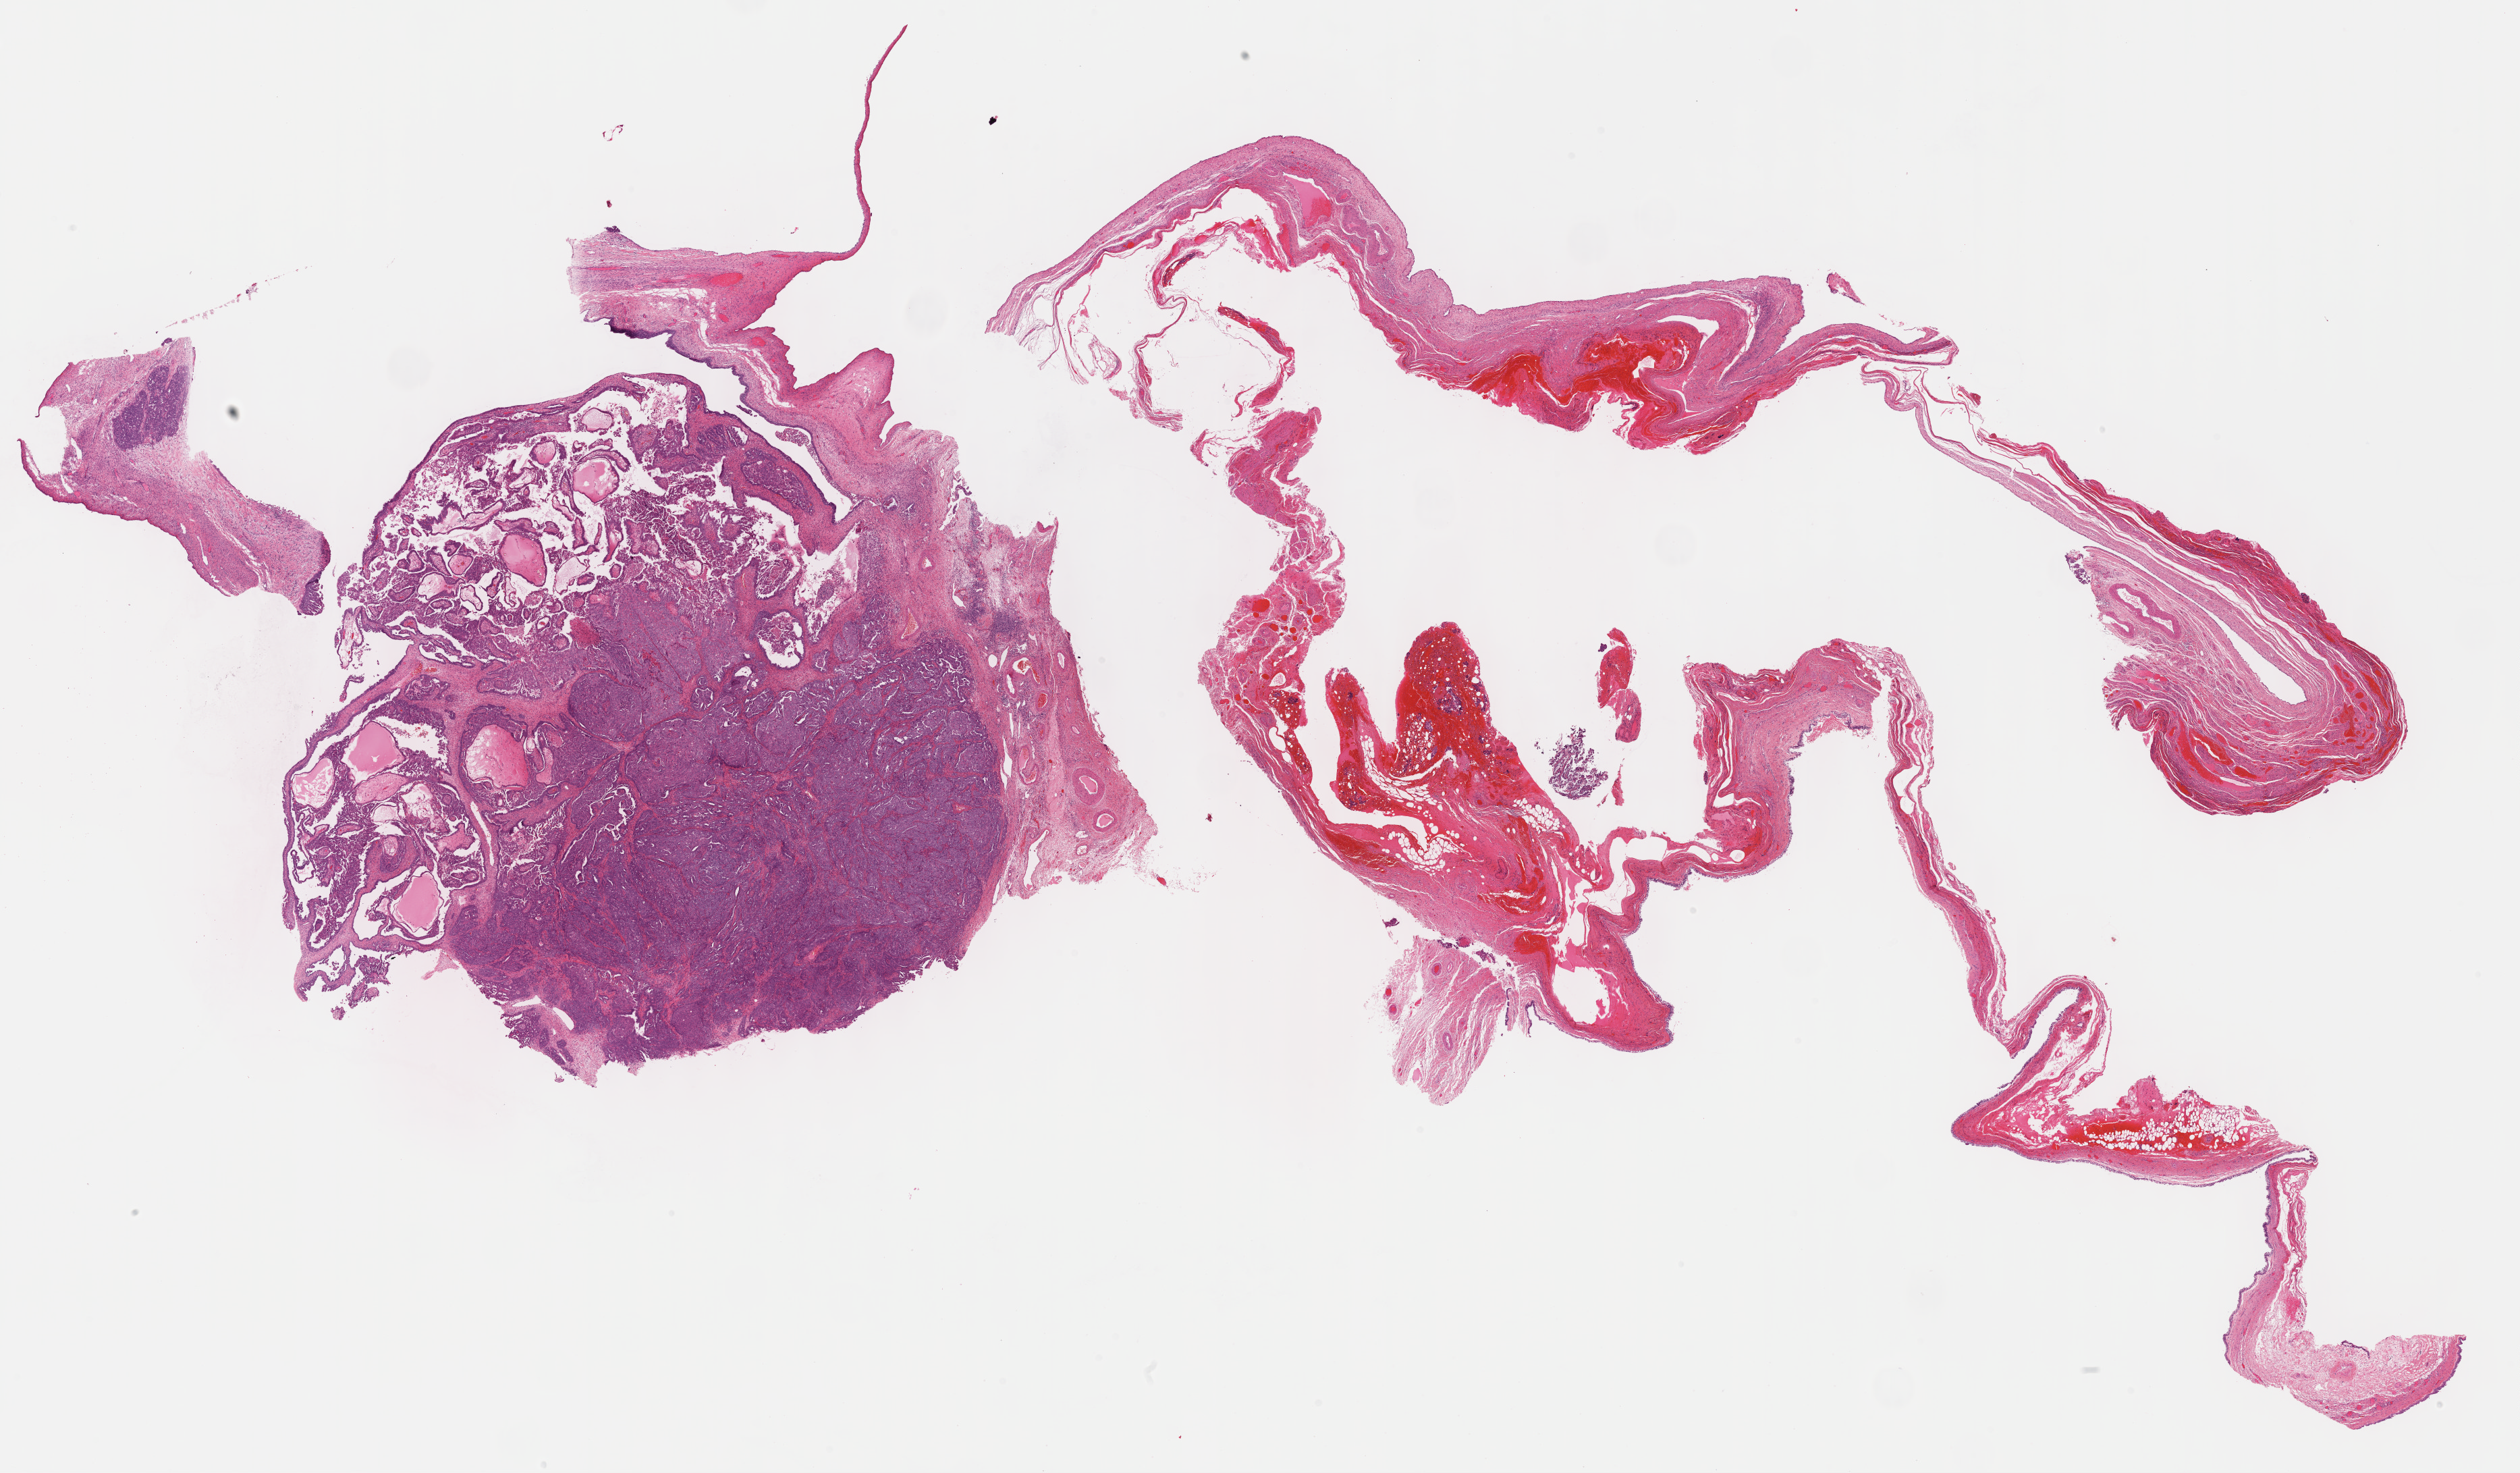
Whole-slide histology image, H&E, shown as a low-resolution overview of the whole scanned area (about 30.2 x 17.6 mm, acquisition: 40x scan); formalin-fixed paraffin-embedded (FFPE) diagnostic section; sample: primary tumour, ovary. Female patient; age at initial diagnosis 74 years.
Diagnosis: Serous cystadenocarcinoma, NOS.